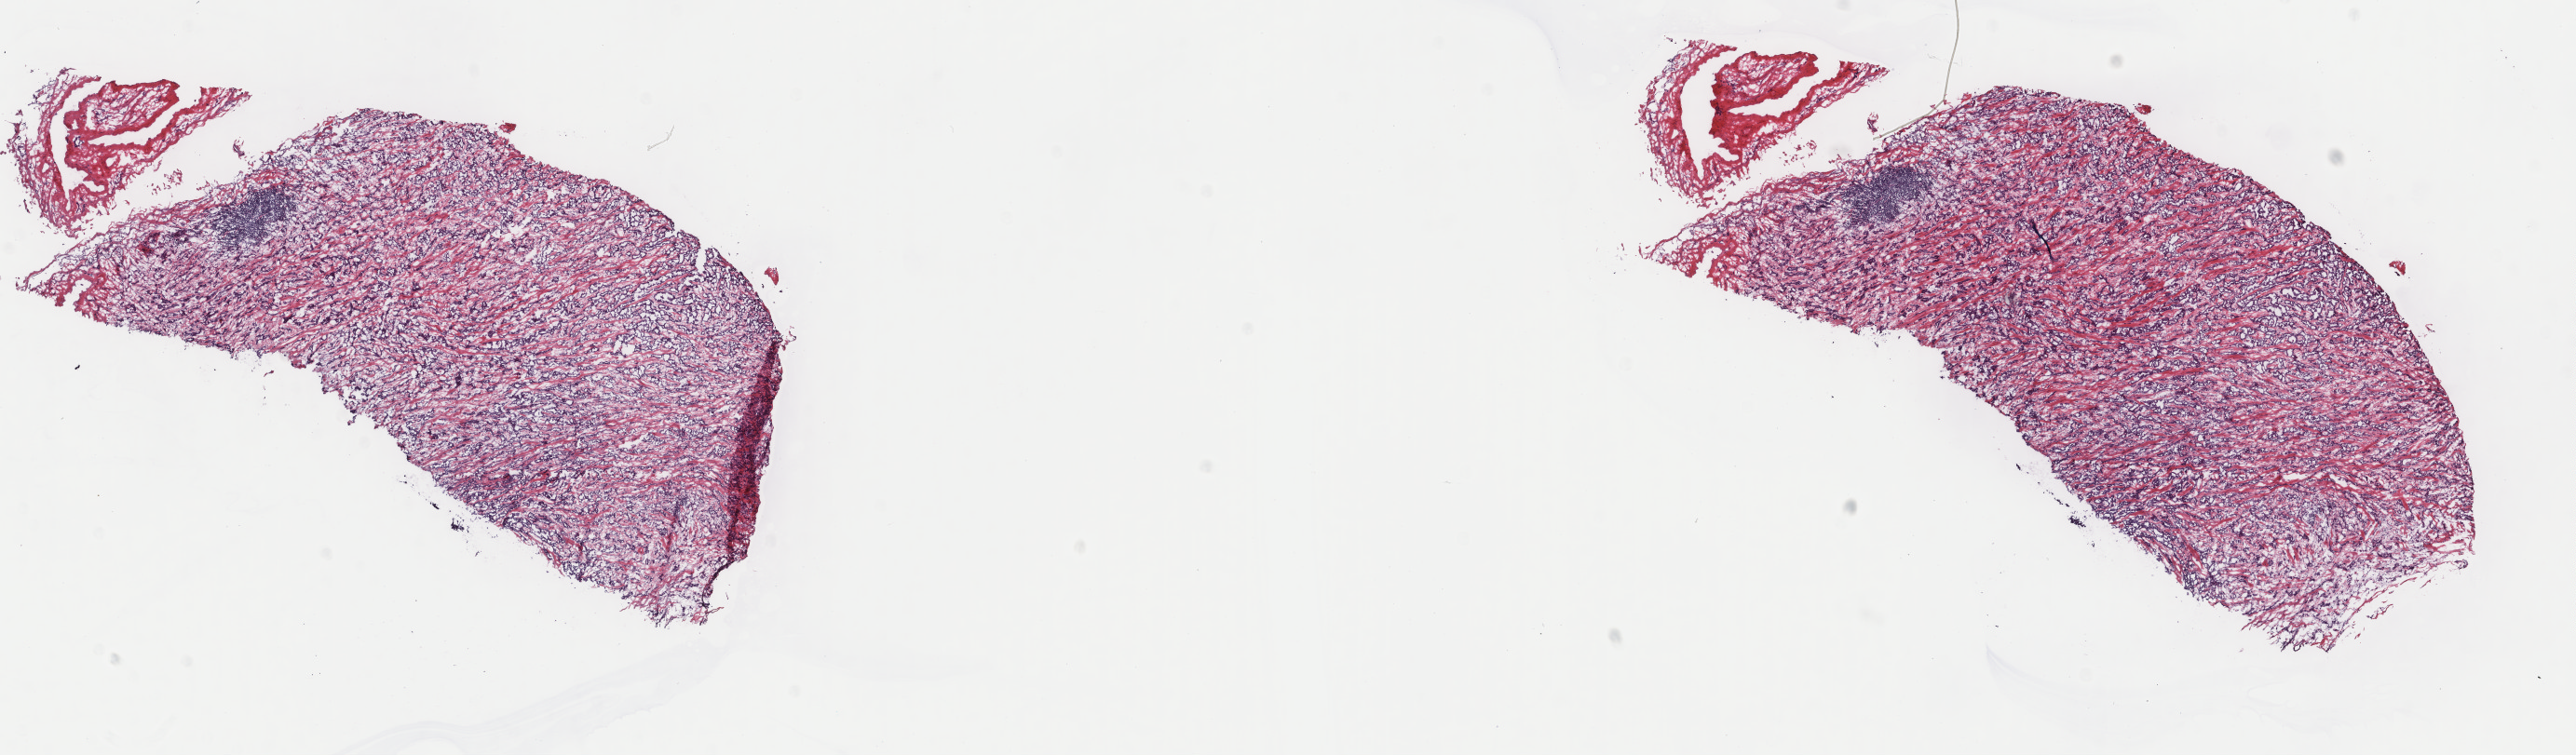
Digitized Hematoxylin and eosin (H&E) stained tissue section (whole slide), shown as a low-resolution overview of the whole scanned area (about 22.0 x 6.4 mm). Frozen section from the top of the tissue portion. Sample: primary tumour, mesothelium. Male, age 55 years at initial diagnosis. Composition of this section per pathologist review: tumour cells 100%, tumour nuclei 80%, normal cells 0%, stromal cells 0%, necrosis 0%. Inflammatory infiltration, as recorded: lymphocyte infiltration 3%, monocyte infiltration 0%, neutrophil infiltration 0%.
TNM: T2 N0 MX. AJCC pathologic stage: II. Diagnosis: Epithelioid mesothelioma, malignant (pleura, NOS).